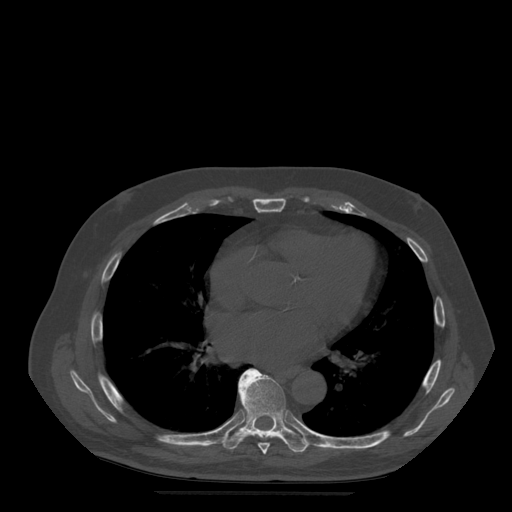
CT including the spine, one axial slice. Slice 320 of 522 in the series (ordered by position). Bone window (W 1800 / L 400 HU). 512 × 512 image matrix. Patient age 72 years. Case-level facts recorded for this patient, not image findings: primary cancer: prostate.
Annotated regions visible in this slice (semi-automatic segmentation, software-assisted and operator-edited):
- T7 vertebra: bounding box <240,390,270,454> (left, top, right, bottom; pixels)
- T8 vertebra: <222,369,310,453>